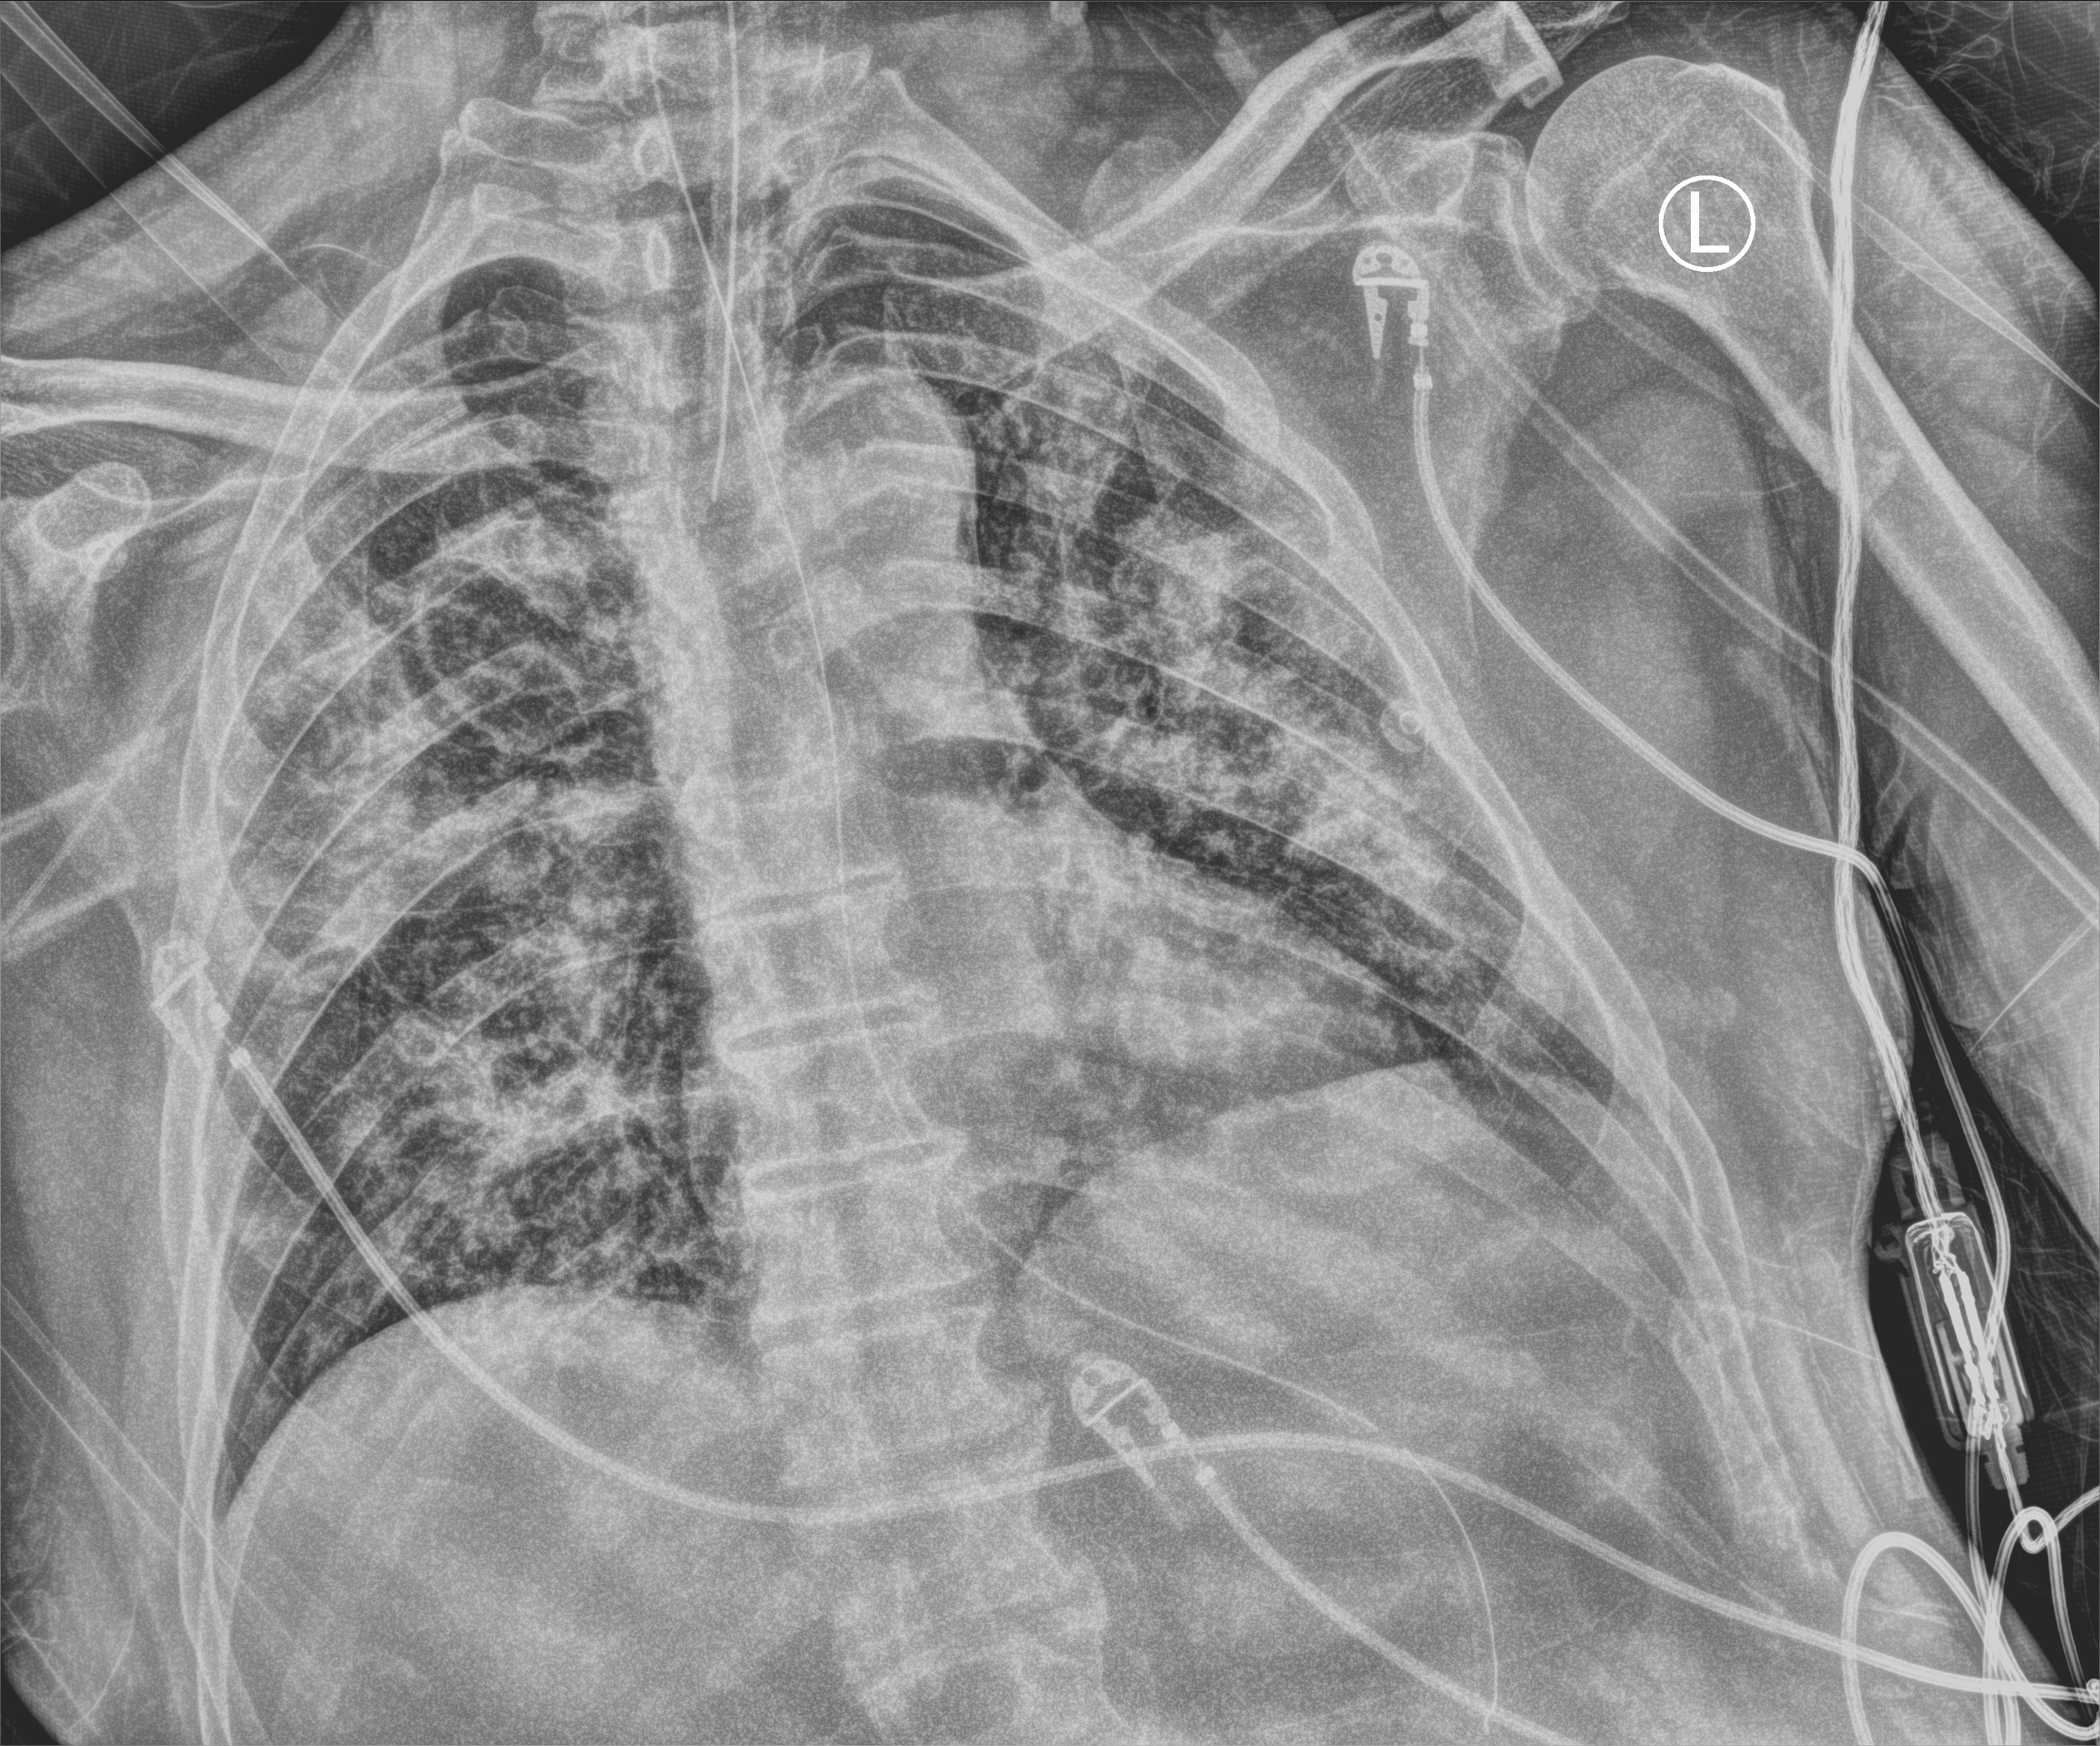
Portable chest radiograph, anteroposterior (AP) projection. Patient hospitalised with COVID-19; male, aged 60–74 years.
Hospital-stay facts (about this admission, not read from this image; timing relative to this image not recorded):
- diabetes (admission record): no
- admitted to intensive care during this hospital stay: yes